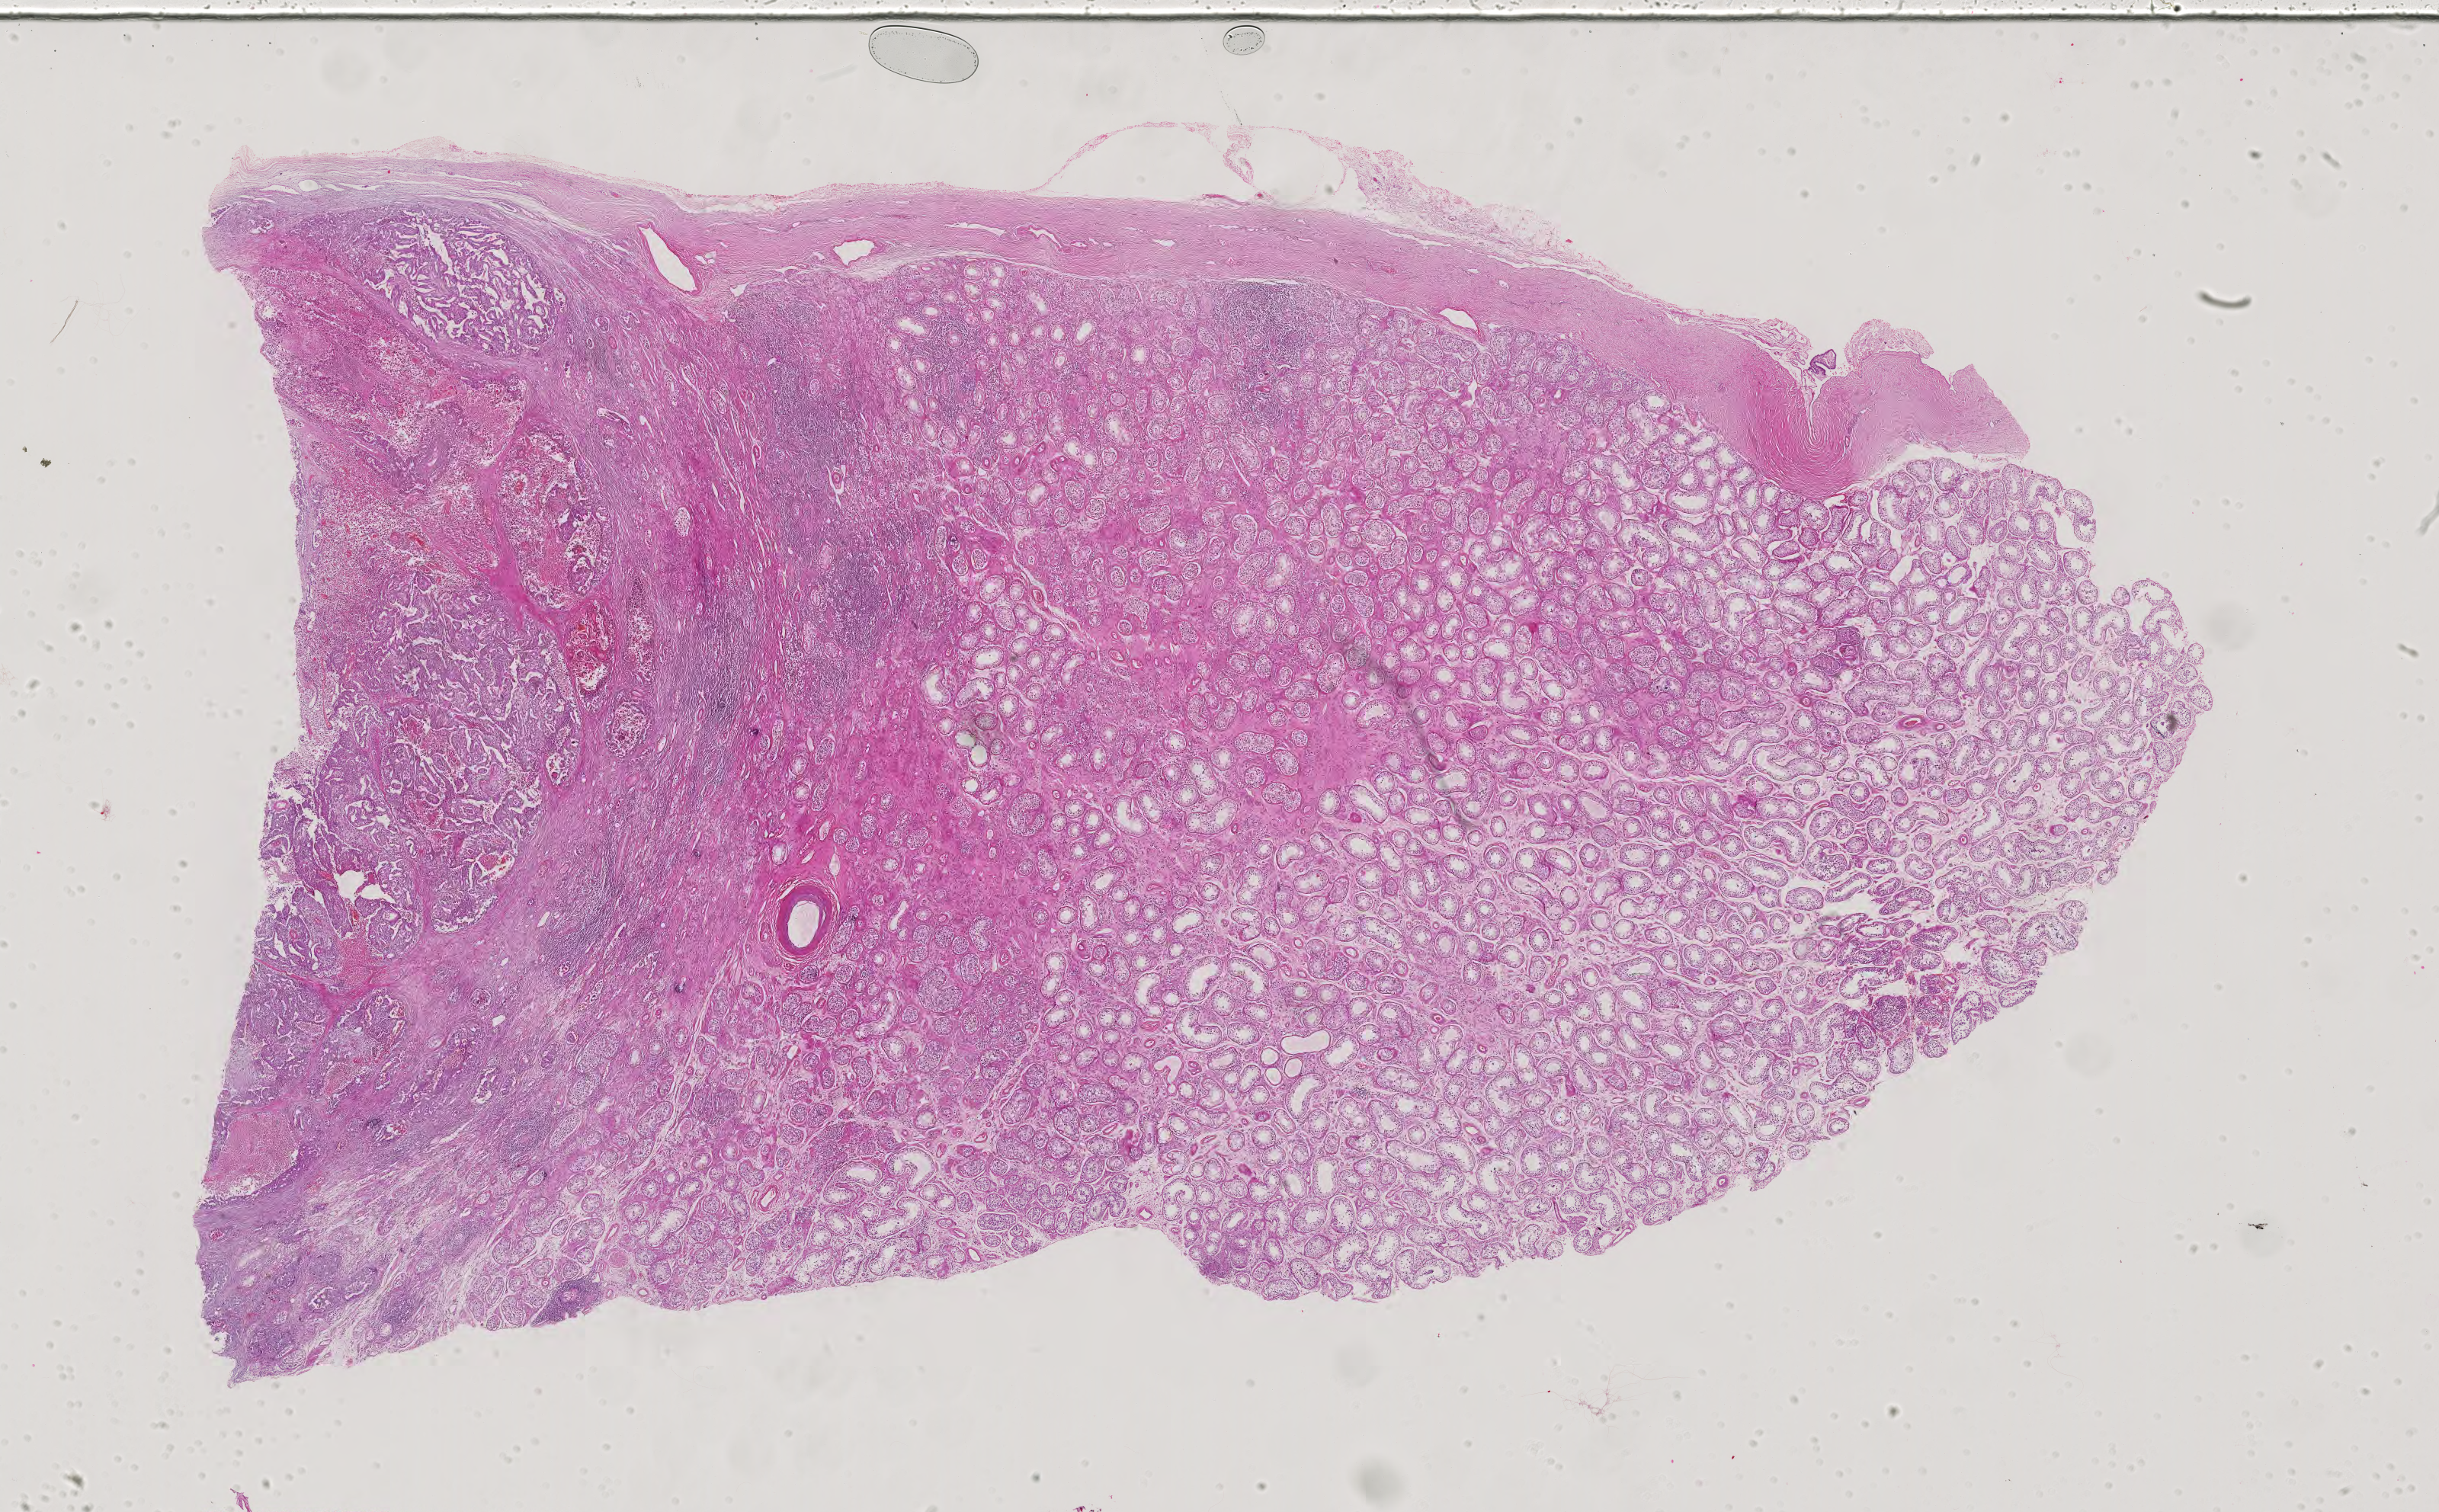
Whole-slide histology image, H&E — shown as a low-resolution overview of the whole scanned area (about 23.3 x 14.5 mm, acquisition: 40x scan), formalin-fixed paraffin-embedded (FFPE) diagnostic section, testis, primary tumour sample. Male, age 41 years at initial diagnosis.
Histologic diagnosis: Embryonal carcinoma, NOS. TNM: T2 N0 M0. AJCC pathologic stage: IS (6th edition).